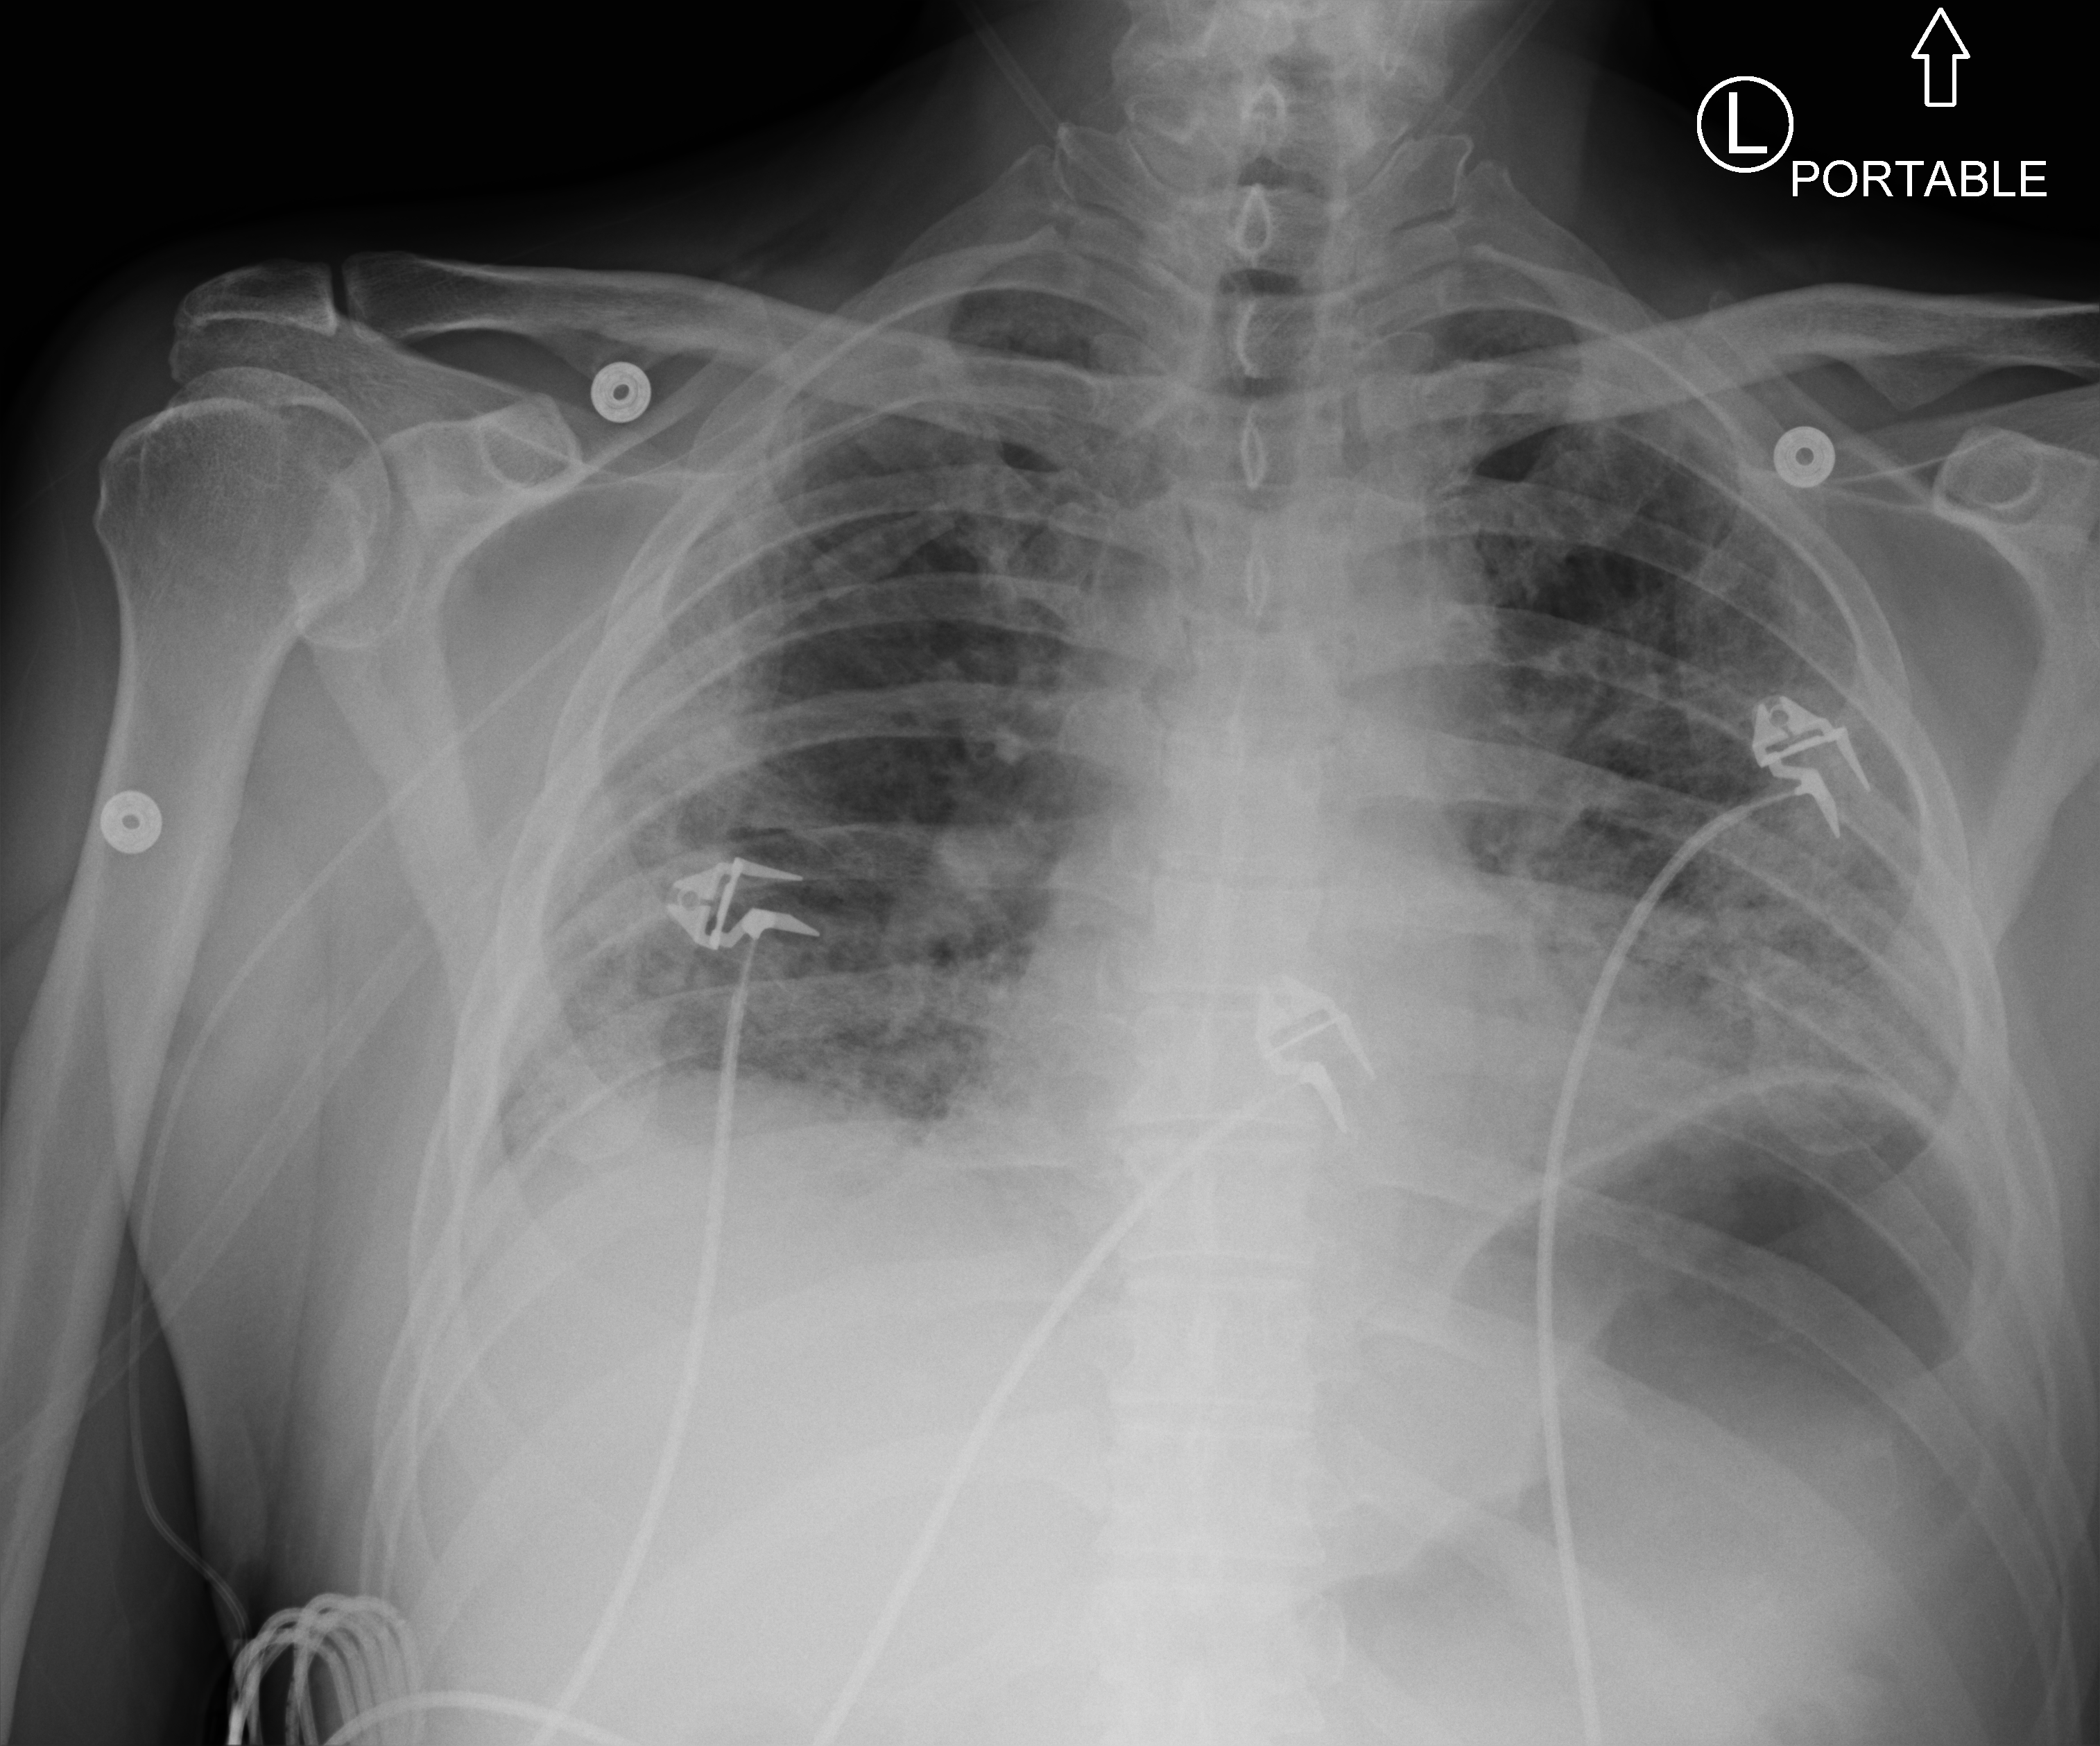
Bedside chest radiograph (computed radiography). Patient hospitalised with COVID-19; male, aged 60–74 years.
From the hospital-stay record, not from the radiograph (when in the stay this image was taken is not recorded): mechanically ventilated during this hospital stay: yes; length of hospital stay: 26 days; chronic kidney disease (admission record): no.